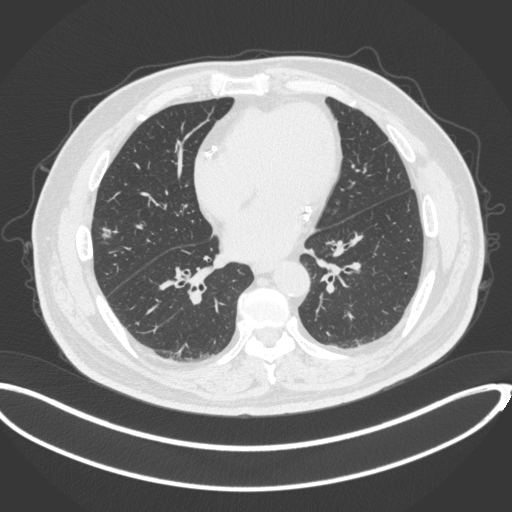
Chest CT, one axial slice; position 135 of 342 along the scan axis; reconstruction kernel B31f; 120 kVp; lung window (W 1500 / L -600 HU); 1 mm slice thickness; 512 × 512 image matrix. Male patient, age 68 years. From the clinical record (not read from this slice): clinical TNM (as recorded): T1c N0 M0.
Annotated regions visible in this slice (rectangle marked by the reading radiologist):
- lung tumour (recorded histology: adenocarcinoma): box from (x=101, y=226) to (x=112, y=240) px